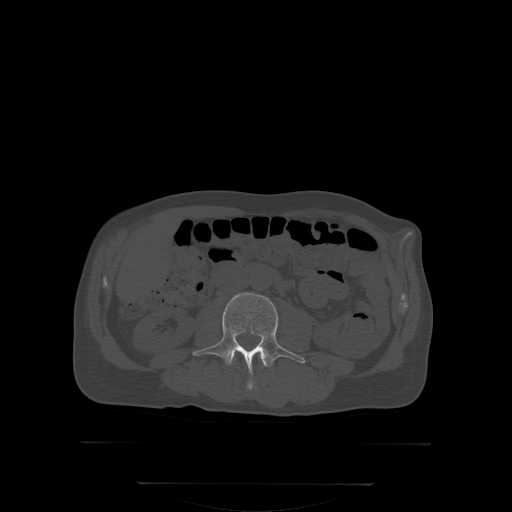
CT including the spine, one axial slice. Slice 125 of 350 in the series (ordered by position). Bone window (W 1800 / L 400 HU). 512 × 512 image matrix. Male patient, age 58 years. From the clinical record (not read from this slice): primary cancer: prostate.
Outlined on this slice (semi-automatically segmented with operator editing):
- L2 vertebra: bounding box [x1, y1, x2, y2] px = [233, 354, 266, 390]
- L3 vertebra: [193, 292, 304, 382]